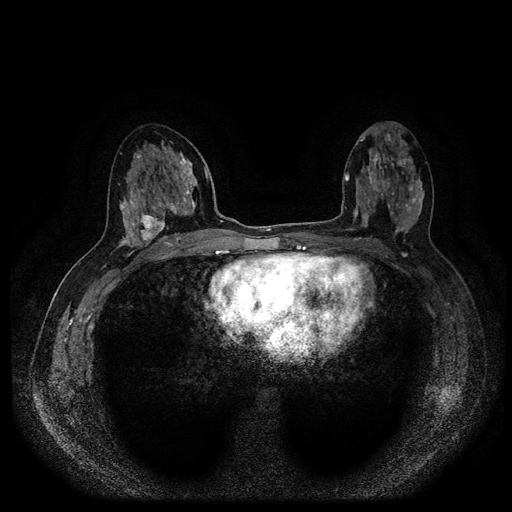
Breast MRI (dynamic contrast-enhanced, multi-phase), one axial slice. Slice 50 of 116 in the series (ordered by position). Dynamic contrast-enhanced series, time point 2 of 5 at this slice position (early post-contrast). 1.5 T. TE 2.6 ms, TR 5.4 ms. 512 × 512 image matrix. Female patient, age 48 years.
Outlined on this slice (semi-automatically segmented with operator editing):
- breast lesion (labelled 'tumour' in the annotation; benign lesions carry a separate 'benign' label): bounding box <136,213,167,247> (left, top, right, bottom; pixels)